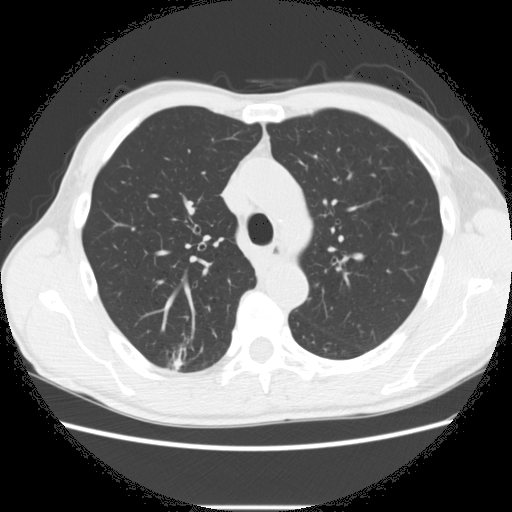
Low-dose screening chest CT, axial slice; second annual screen; lung window (W 1500 / L -600 HU); 2.5 mm slice thickness; 512 × 512 image matrix. Male, age 66 years at enrolment.
- Lesion marked by an expert reader, bounding box (x1, y1, x2, y2) in pixels: (163, 341, 220, 381).
- The screening reader recorded 5 non-calcified nodules or masses ≥4 mm on this exam; which of them this box marks is not recorded.
- Later outcome: lung cancer diagnosed 75 days after this screen — adenocarcinoma, NOS, right upper lobe, undifferentiated (G4), stage IA (AJCC 6th edition), 20 mm at pathology.